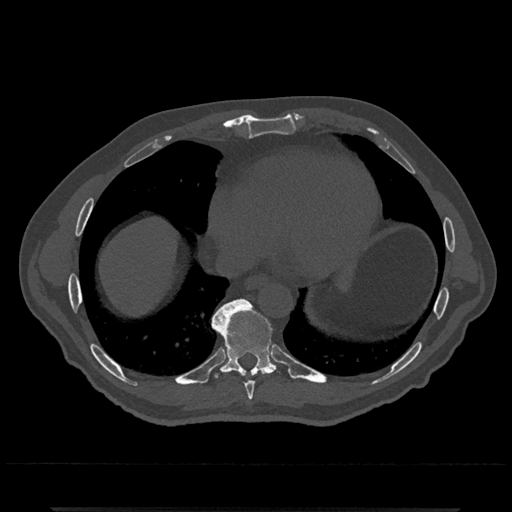
CT including the spine, one axial slice; slice 632 of 797 in the series (ordered by position); 120 kVp; bone window (W 1800 / L 400 HU); 0.5 mm slice thickness; 512 × 512 image matrix, field of view 393 × 393 mm. Patient: male, 67 years. From the clinical record (not read from this slice): primary cancer: prostate.
Outlined on this slice (semi-automatic segmentation, software-assisted and operator-edited):
- T8 vertebra: bounding box [x1, y1, x2, y2] px = [245, 381, 254, 400]
- T9 vertebra: [212, 299, 282, 383]